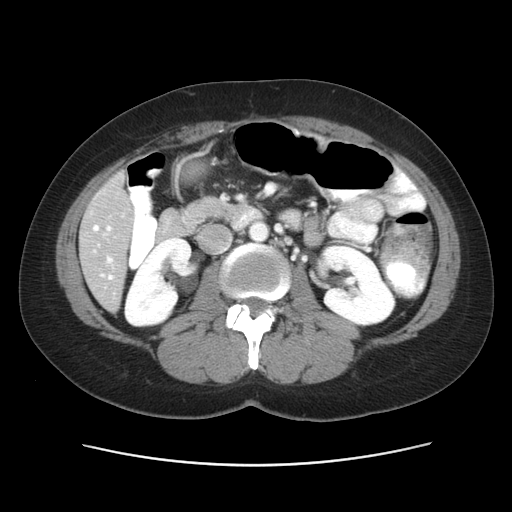
Contrast-enhanced abdominal CT, one axial slice. Slice 20 of 52 in the series (ordered by position). Reconstruction kernel STANDARD. 120 kVp. Intravenous contrast given. Soft-tissue window (W 400 / L 40 HU). 5 mm slice thickness. 512 × 512 image matrix, field of view 362 × 362 mm. Female patient, age 48 years. Case-level facts recorded for this patient, not image findings: diagnosis: colorectal cancer liver metastases, imaged before liver resection; multiple liver metastases: yes; largest metastasis: 4.5 cm.
Outlined on this slice (outlined manually by an expert reader):
- hepatic veins: bounding box [x1, y1, x2, y2] px = [94, 215, 124, 279]
- liver: [80, 178, 132, 309]
- portal vein (with intrahepatic branches): [106, 226, 113, 263]